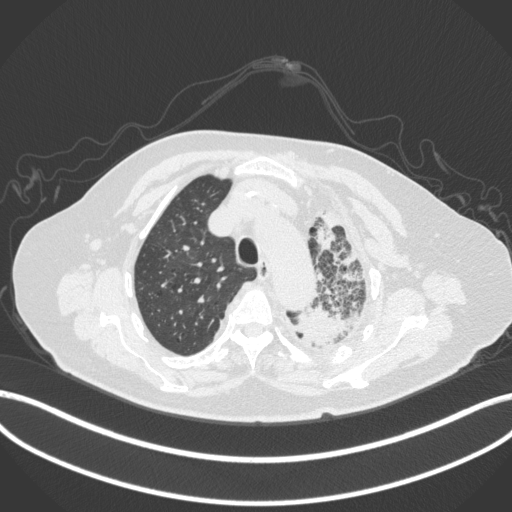
Chest CT, one axial slice; position 307 of 399 along the scan axis; 120 kVp; lung window (W 1500 / L -600 HU); 1 mm slice thickness; 512 × 512 image matrix, field of view 400 × 400 mm. Female patient, age 75 years. From the clinical record (not read from this slice): clinical TNM (as recorded): T3 N3 M1.
Outlined on this slice (rectangle marked by the reading radiologist):
- lung tumour (recorded histology: adenocarcinoma): bounding box (x1, y1, x2, y2) in pixels: (293, 300, 358, 347)